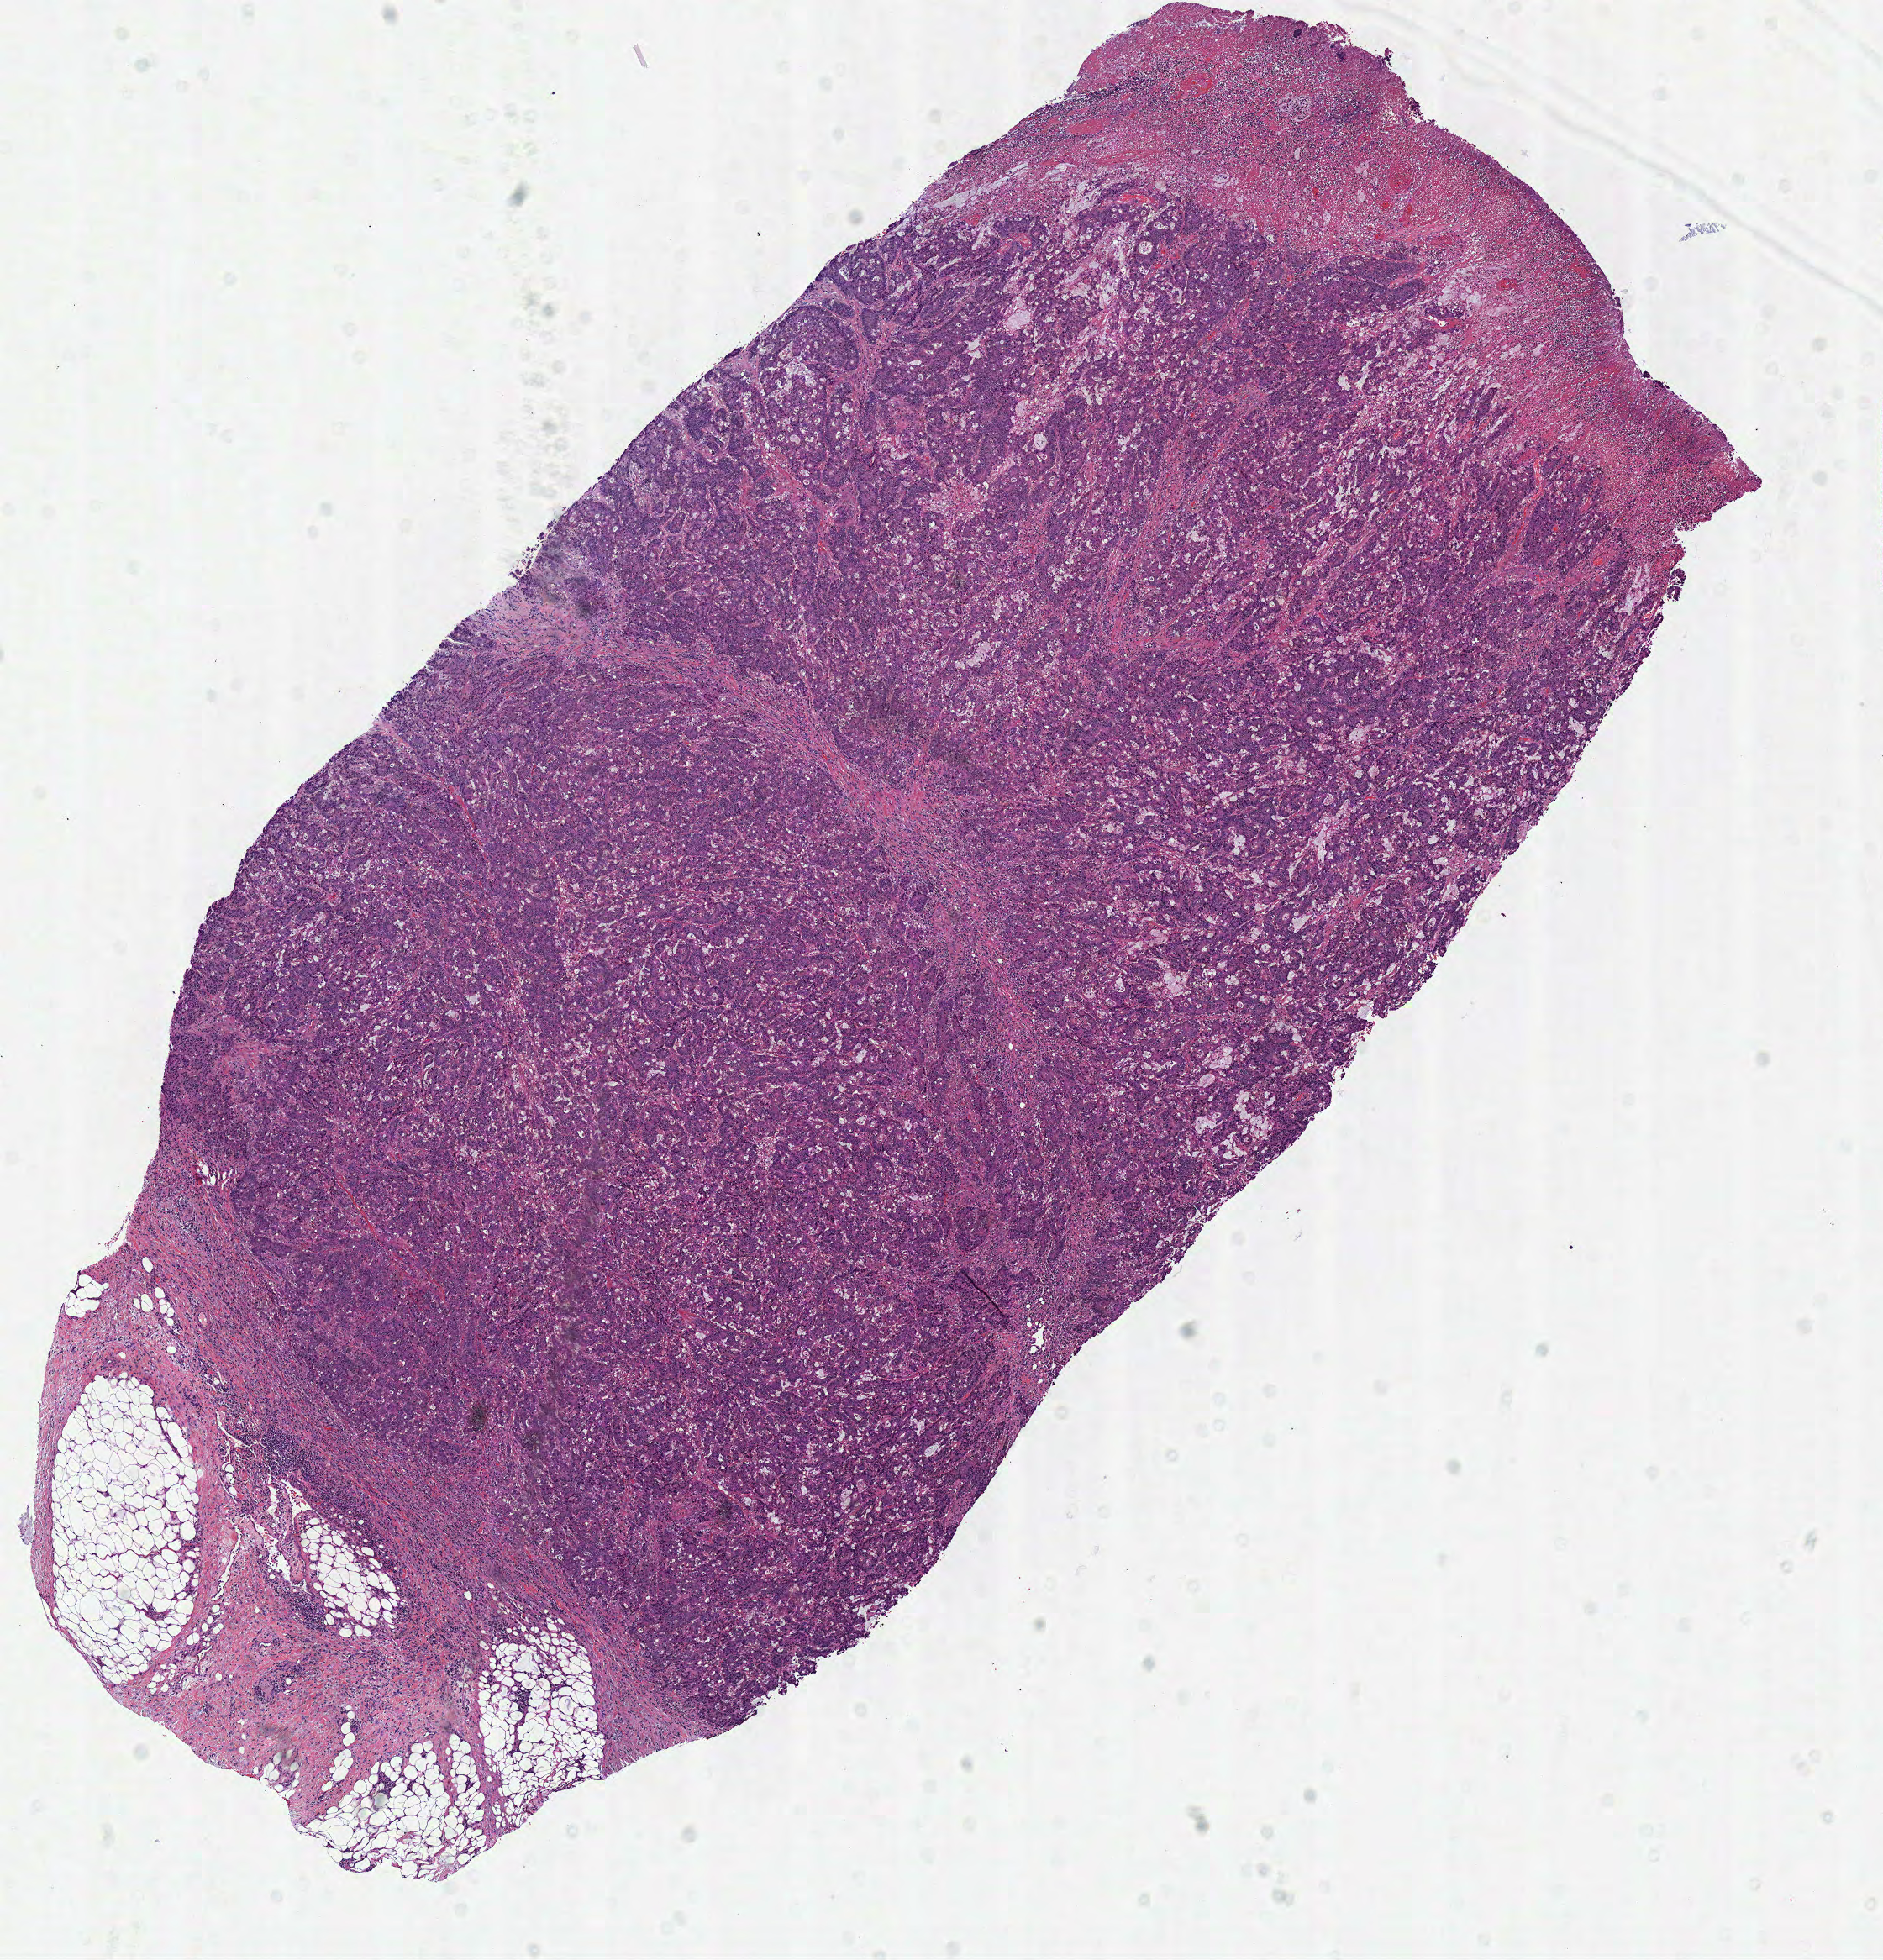
Hematoxylin and eosin (H&E) stained whole-slide image — a low-resolution overview of the entire scanned area, about 8.8 x 9.2 mm; frozen section from the top of the tissue portion; sample: primary tumour, colon. Patient: male, age at initial diagnosis 74 years. Pathologist review of this section (percent, as recorded): tumour cells 90%, tumour nuclei 80%, normal cells 0%, stromal cells 9%, necrosis 1%. Inflammatory infiltration, as recorded: lymphocyte infiltration 10%, monocyte infiltration 0%, neutrophil infiltration 1%.
- AJCC pathologic stage: IIA
- lymph nodes positive (case pathology): 0 of 18 examined
- histologic diagnosis: Mucinous adenocarcinoma (ascending colon)